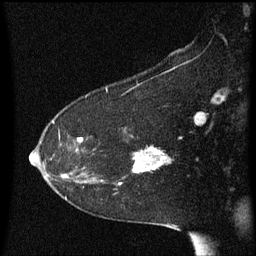
Breast MRI (dynamic contrast-enhanced), one sagittal slice; slice 39 of 60 in the series (ordered by position); dynamic contrast-enhanced series, image 2 of 3 at this slice position (ordered by acquisition); 1.5 T; TE 4.2 ms, TR 8.4 ms; 2 mm slice thickness; 256 × 256 image matrix, field of view 200 × 200 mm. Patient: female, 54 years. Case-level facts recorded for this patient, not image findings: setting: breast cancer imaged before/during neoadjuvant chemotherapy; receptor status: HR-positive, HER2-negative.
Annotated regions visible in this slice (semi-automatically segmented with operator editing):
- analysis volume of interest (the breast-tissue region the enhancement analysis was run in; not a lesion): bounding box <117,132,176,185> (left, top, right, bottom; pixels)
- tumour enhancement mask (voxels above the 70 % enhancement threshold inside the analysis volume of interest): <121,146,166,185>